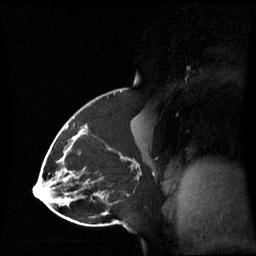
Breast MRI (dynamic contrast-enhanced), one sagittal slice. Slice 35 of 60 in the series (ordered by position). Dynamic contrast-enhanced series, image 2 of 3 at this slice position (ordered by acquisition). 1.5 T. TE 4.2 ms, TR 8.4 ms. 2.8 mm slice thickness. 256 × 256 image matrix, field of view 270 × 270 mm. Female patient, age 43 years. From the clinical record (not read from this slice): setting: breast cancer imaged before/during neoadjuvant chemotherapy; receptor status: triple-negative.
Outlined on this slice (semi-automatically segmented with operator editing):
- analysis volume of interest (the breast-tissue region the enhancement analysis was run in; not a lesion): bounding box (x1, y1, x2, y2) in pixels: (65, 118, 143, 198)
- tumour enhancement mask (voxels above the 70 % enhancement threshold inside the analysis volume of interest): (65, 125, 129, 174)